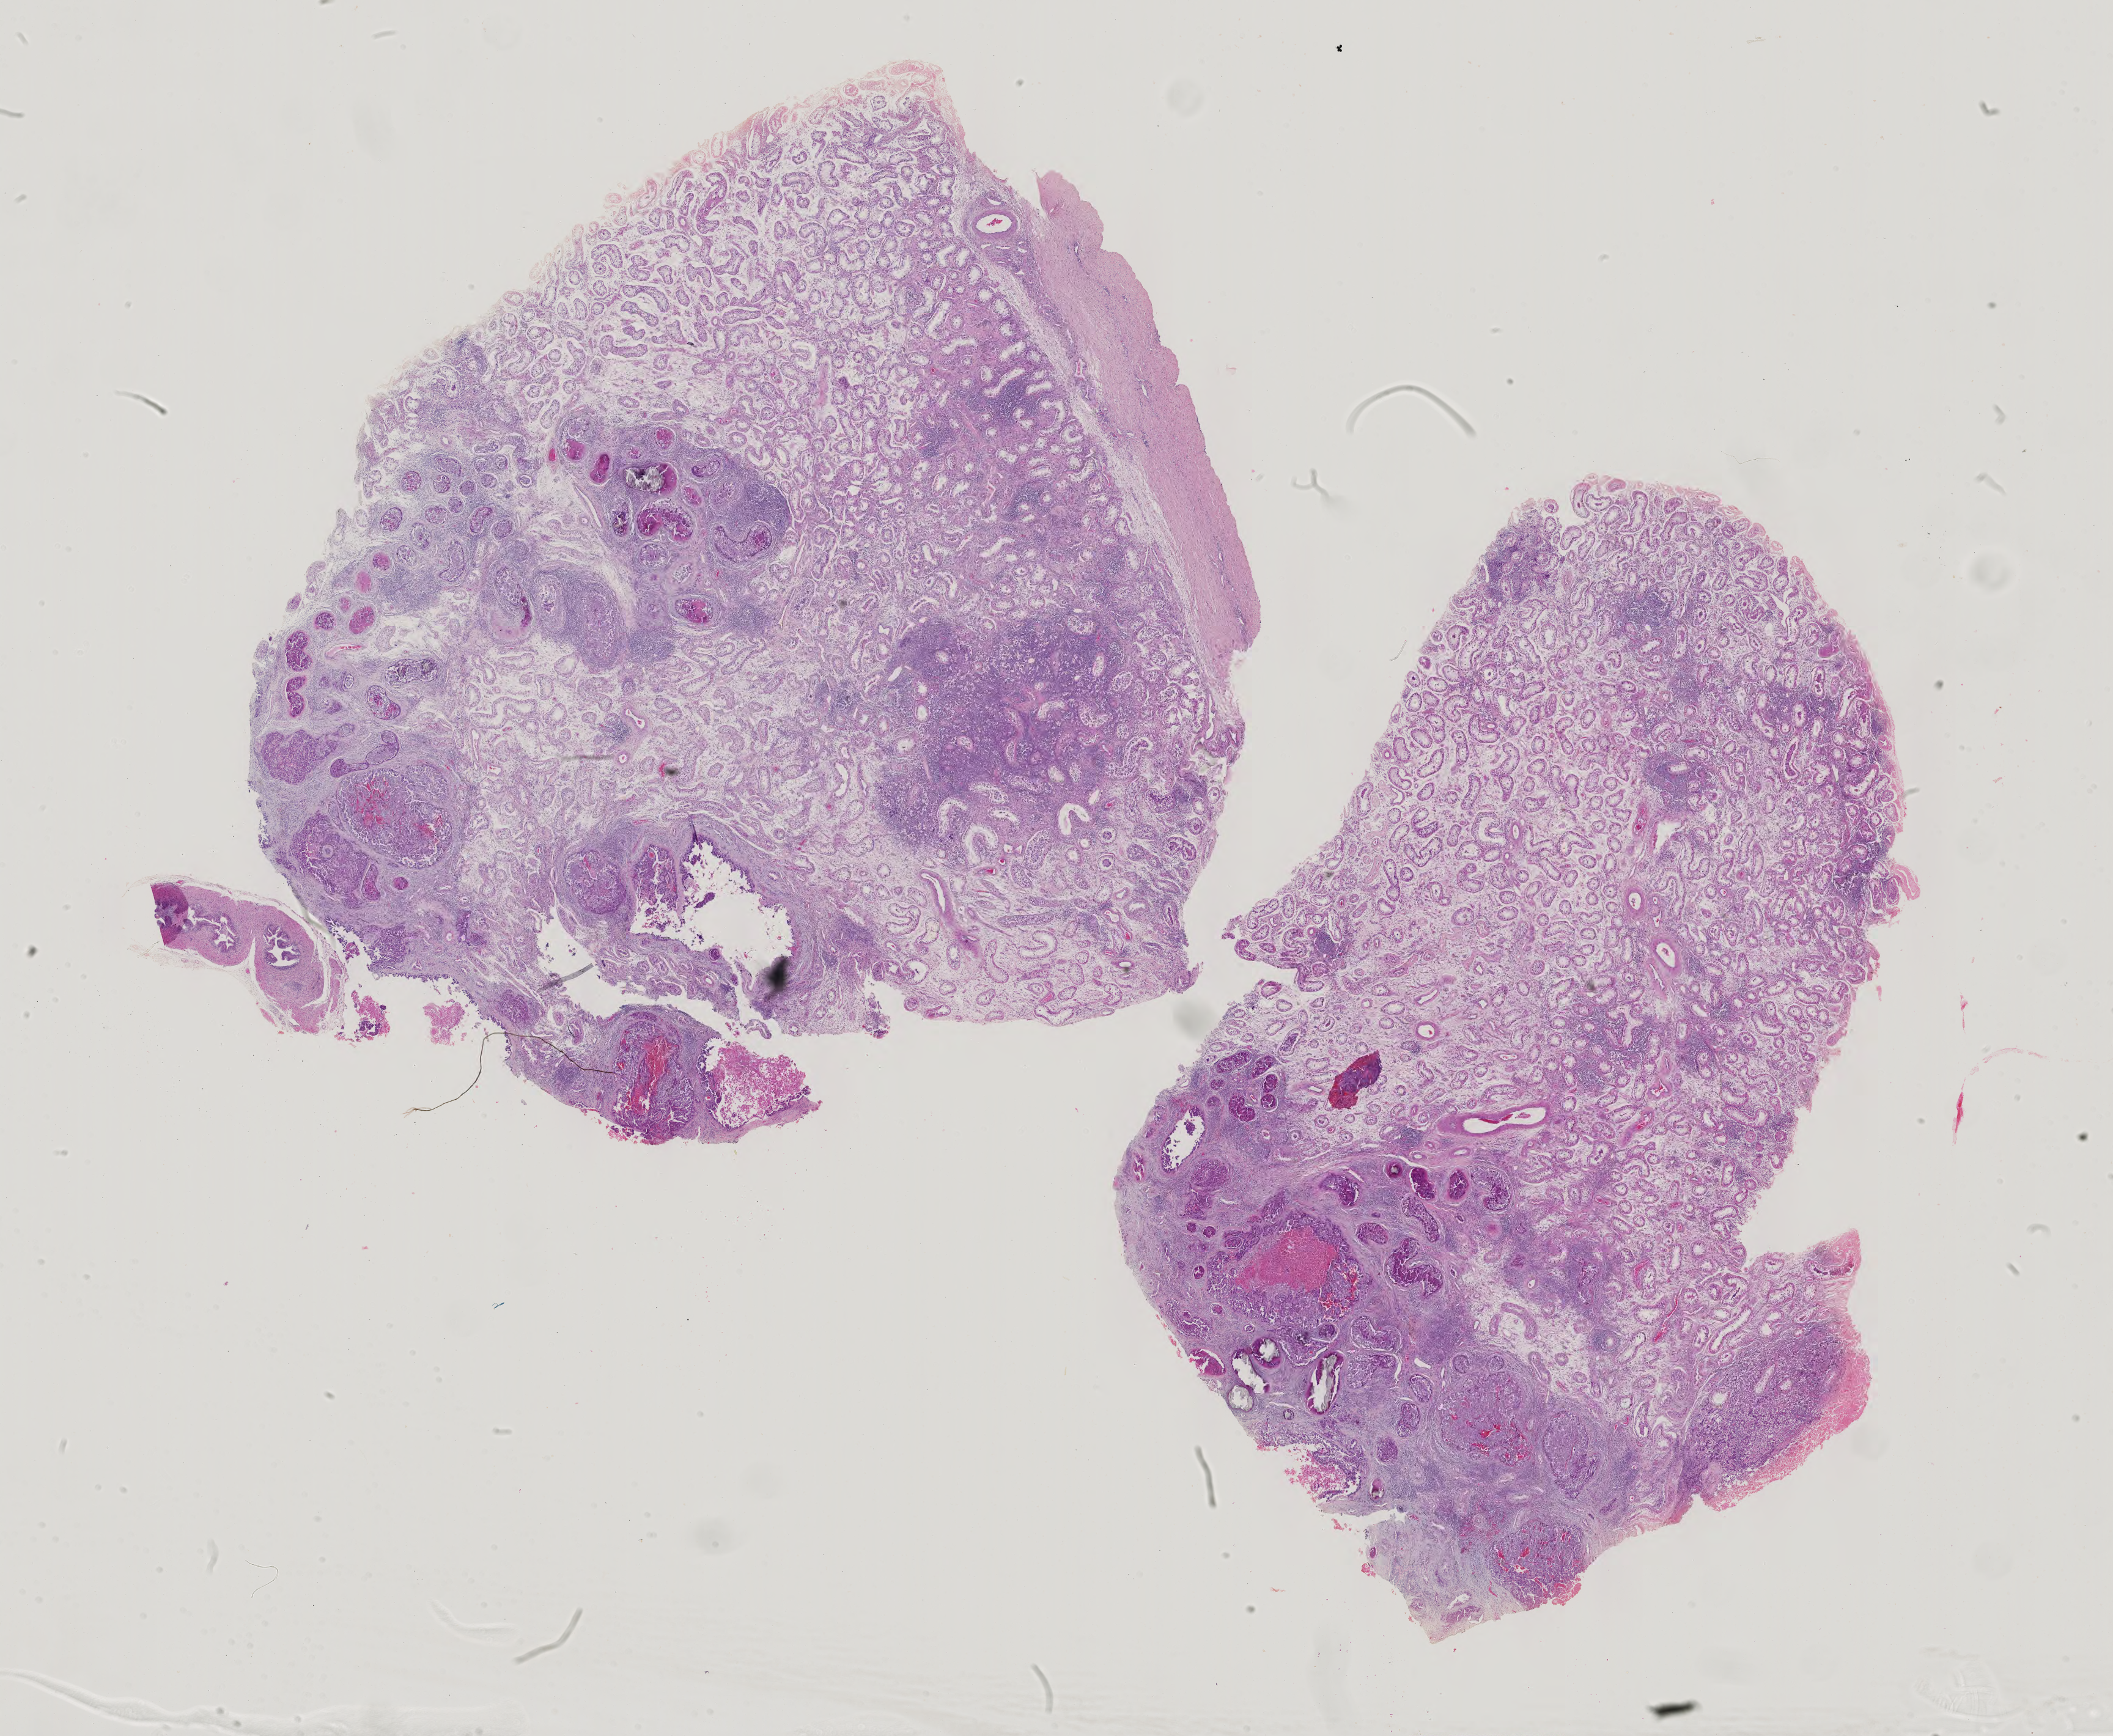
Digitized H&E-stained tissue section (whole slide), shown as a low-resolution overview of the whole scanned area (about 25.2 x 20.7 mm, from a 40x scan). Formalin-fixed paraffin-embedded (FFPE) diagnostic section. Sample: primary tumour, testis. Male, age 19 years at initial diagnosis.
TNM: T1 NX M0. Diagnosis: Embryonal carcinoma, NOS. AJCC pathologic stage: II (4th edition). Laterality: right.